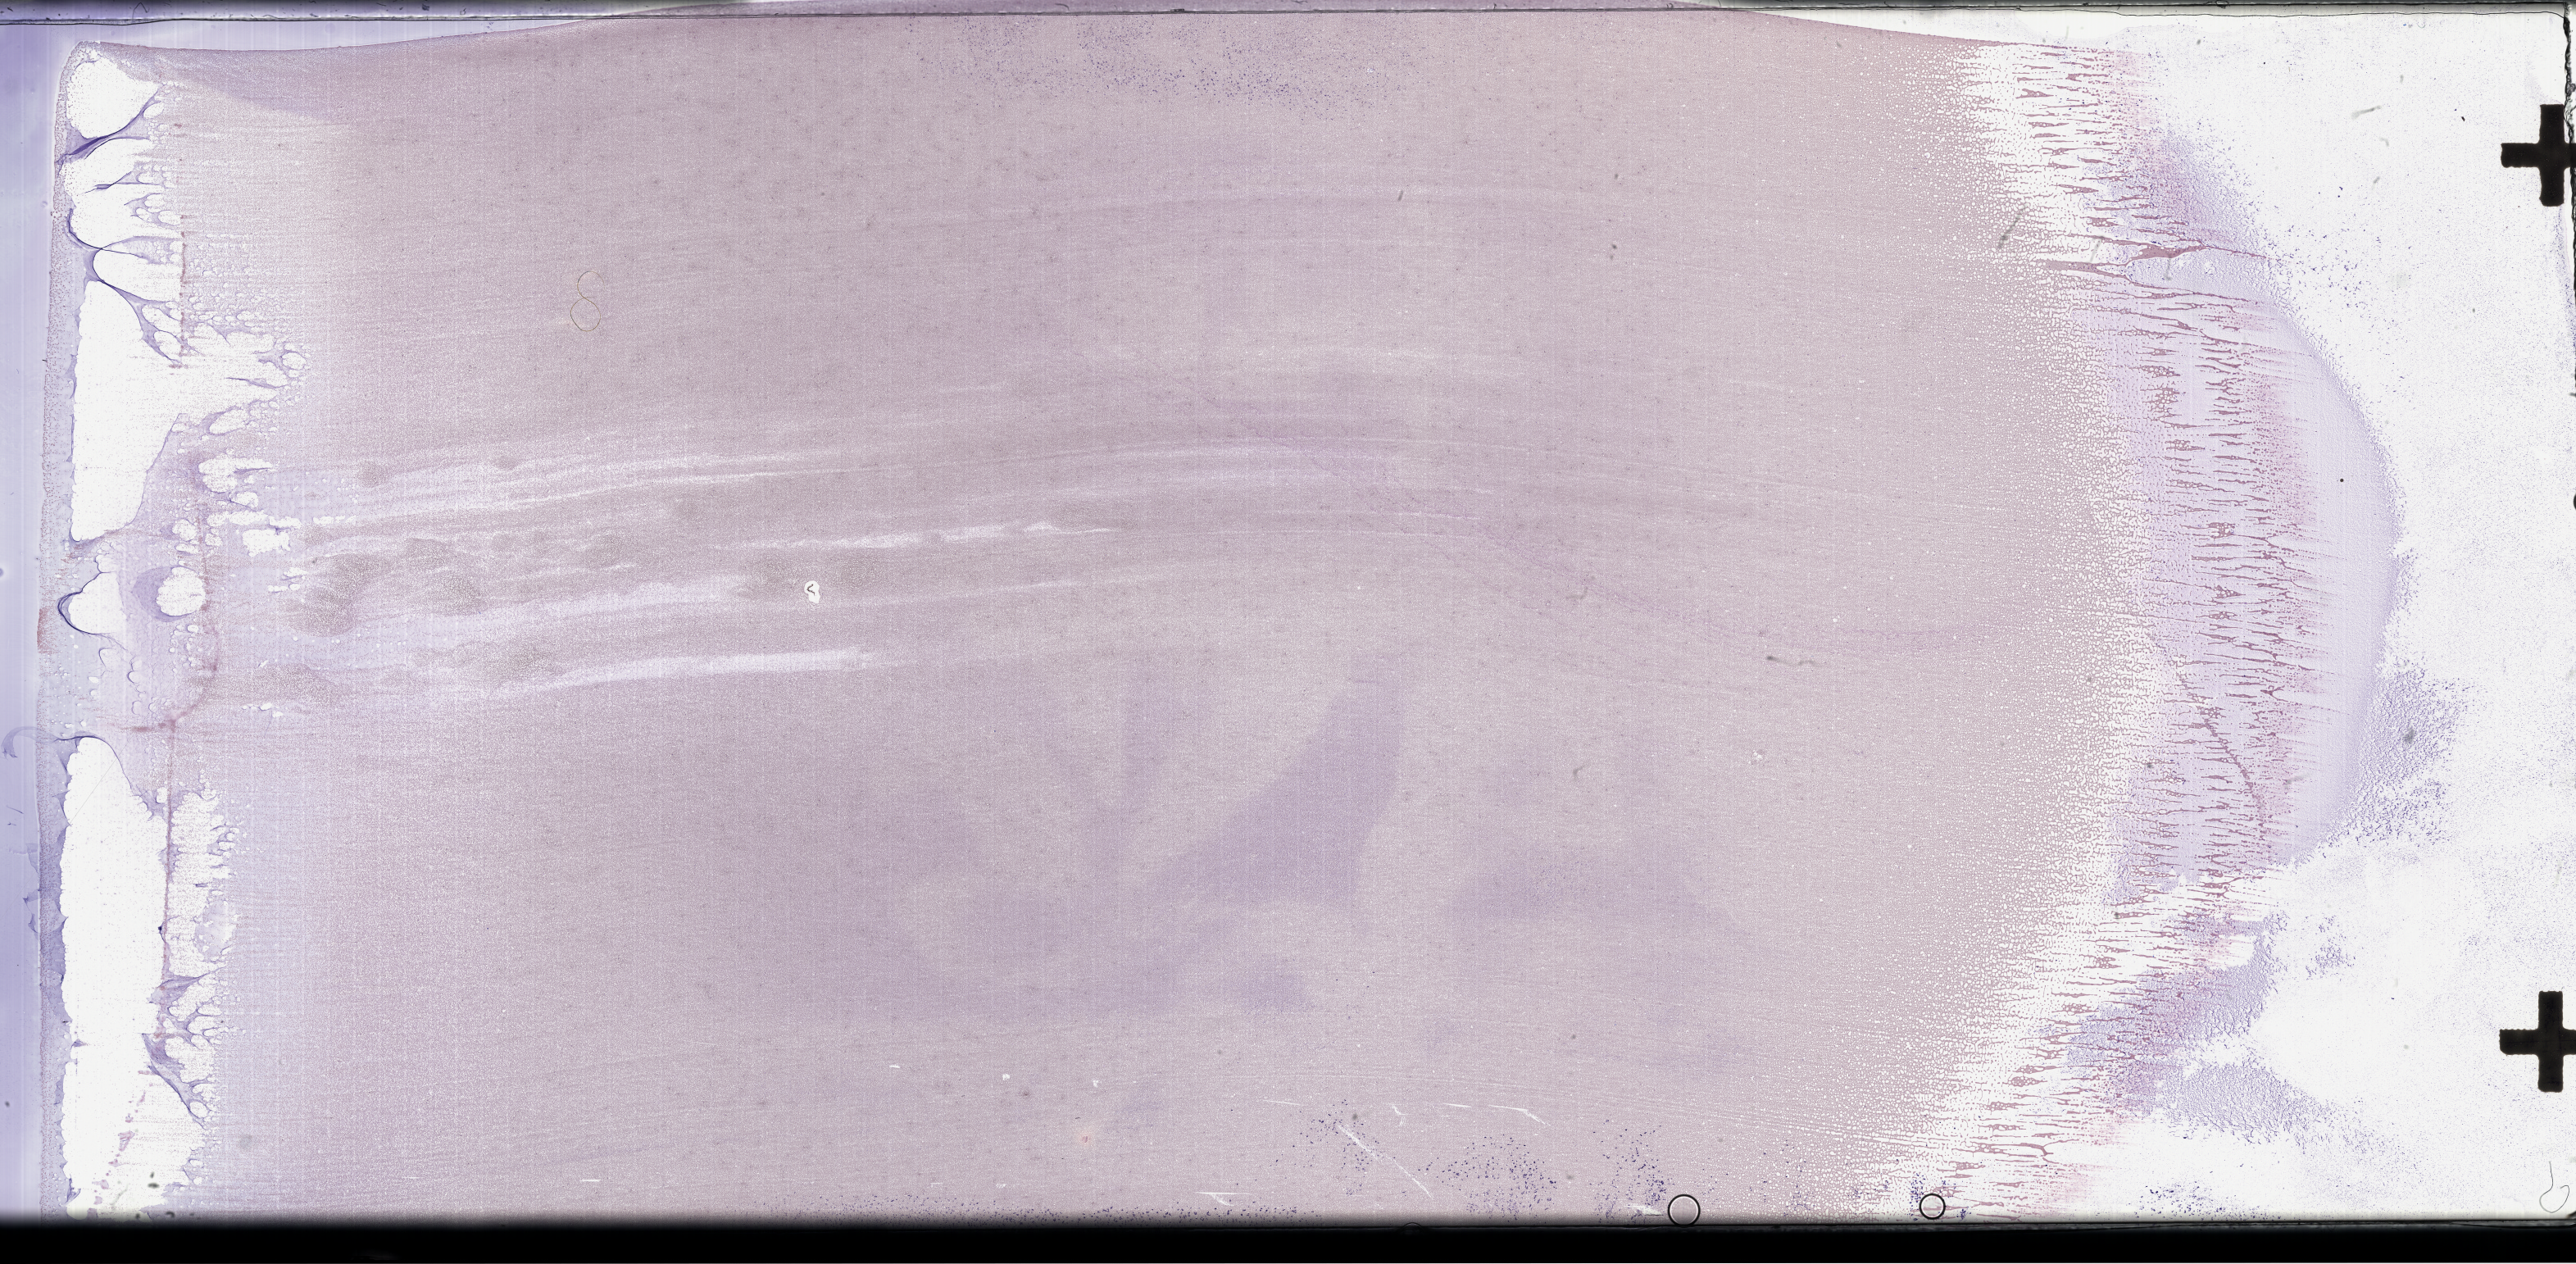
Wright–Giemsa-stained whole blood smear, whole-slide image — whole scanned area (about 50.8 x 24.9 mm) shown as a low-resolution overview, specimen time point: collected on treatment. Patient: female.
* patient diagnosis: Plasma Cell Myeloma